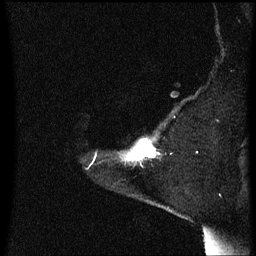
Breast MRI (dynamic contrast-enhanced), one sagittal slice. Position 53 of 60 along the scan axis. Dynamic contrast-enhanced series, image 2 of 3 at this slice position (ordered by acquisition). 1.5 T. TE 4.2 ms, TR 8.4 ms. 256 × 256 image matrix, field of view 200 × 200 mm. Female patient, age 54 years. Case-level facts recorded for this patient, not image findings: setting: breast cancer imaged before/during neoadjuvant chemotherapy; receptor status: HR-positive, HER2-negative.
Outlined on this slice (semi-automatic segmentation, software-assisted and operator-edited):
- analysis volume of interest (the breast-tissue region the enhancement analysis was run in; not a lesion): bounding box <125,140,158,167> (left, top, right, bottom; pixels)
- tumour enhancement mask (voxels above the 70 % enhancement threshold inside the analysis volume of interest): <132,140,156,161>